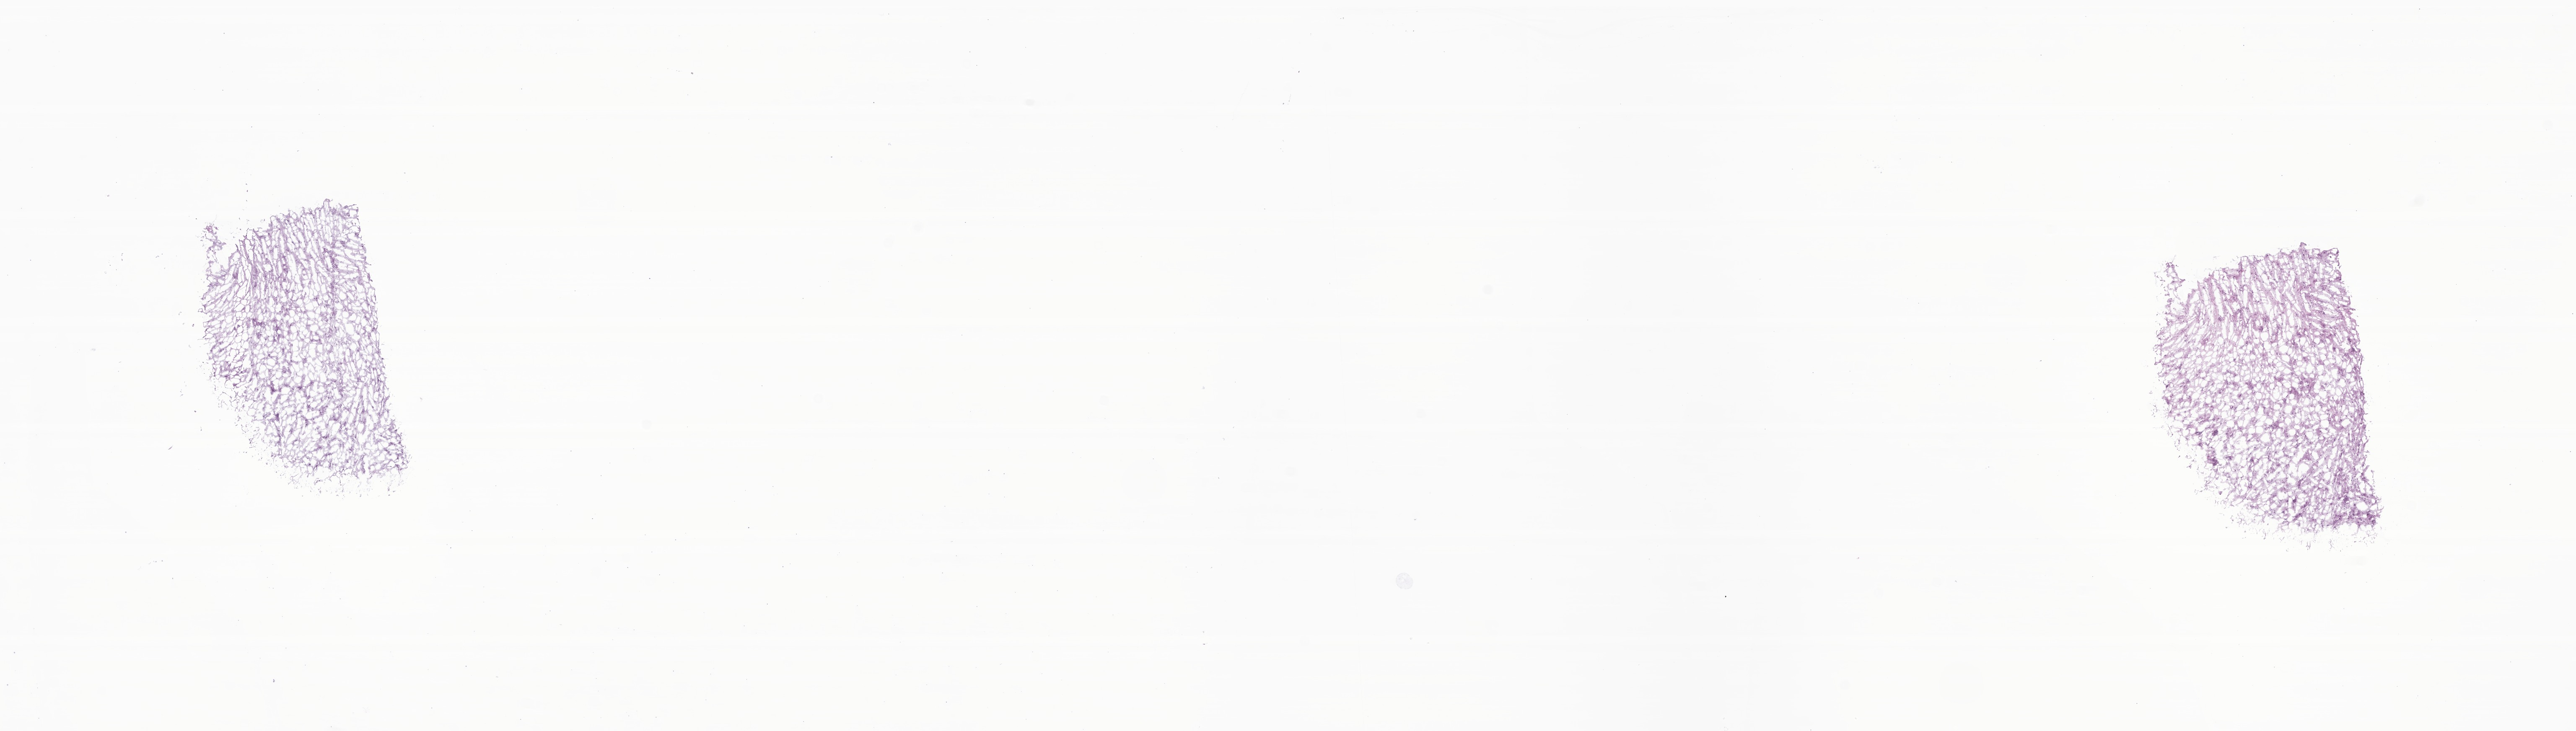
Whole-slide image, H&E stain of tumor tissue from the brain — whole scanned area (about 25.9 x 7.4 mm) shown as a low-resolution overview. Cryosection (OCT / tissue freezing medium). Patient: male, age 189 months (15 years 9 months).
Diagnosis: Neoplasm, malignant.